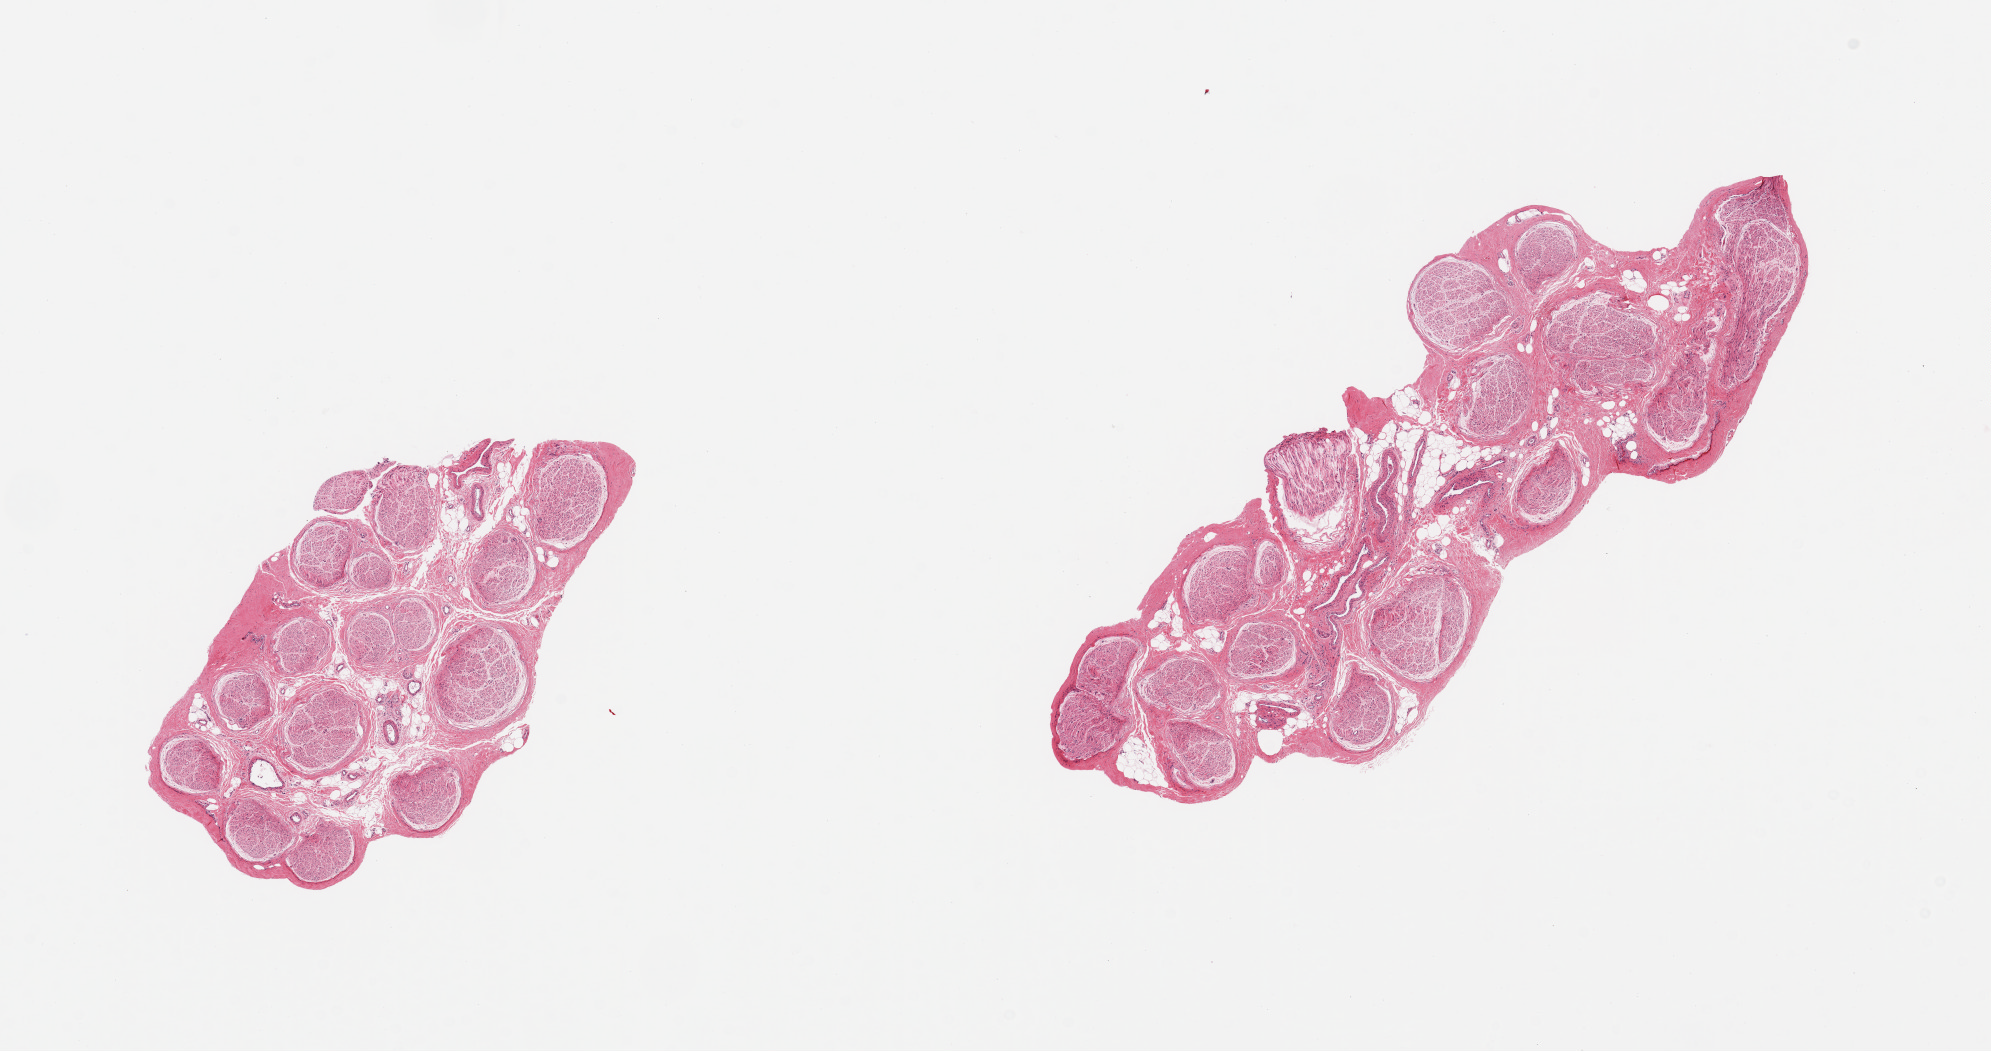
H&E whole-slide image, low-resolution overview of the scanned area, about 15.8 x 8.3 mm. PAXgene-fixed, paraffin-embedded tissue. Target tissue: tibial nerve. Tissue donor sample. Donor: male.
Review note (as recorded): 2 pieces, no adherent fat.